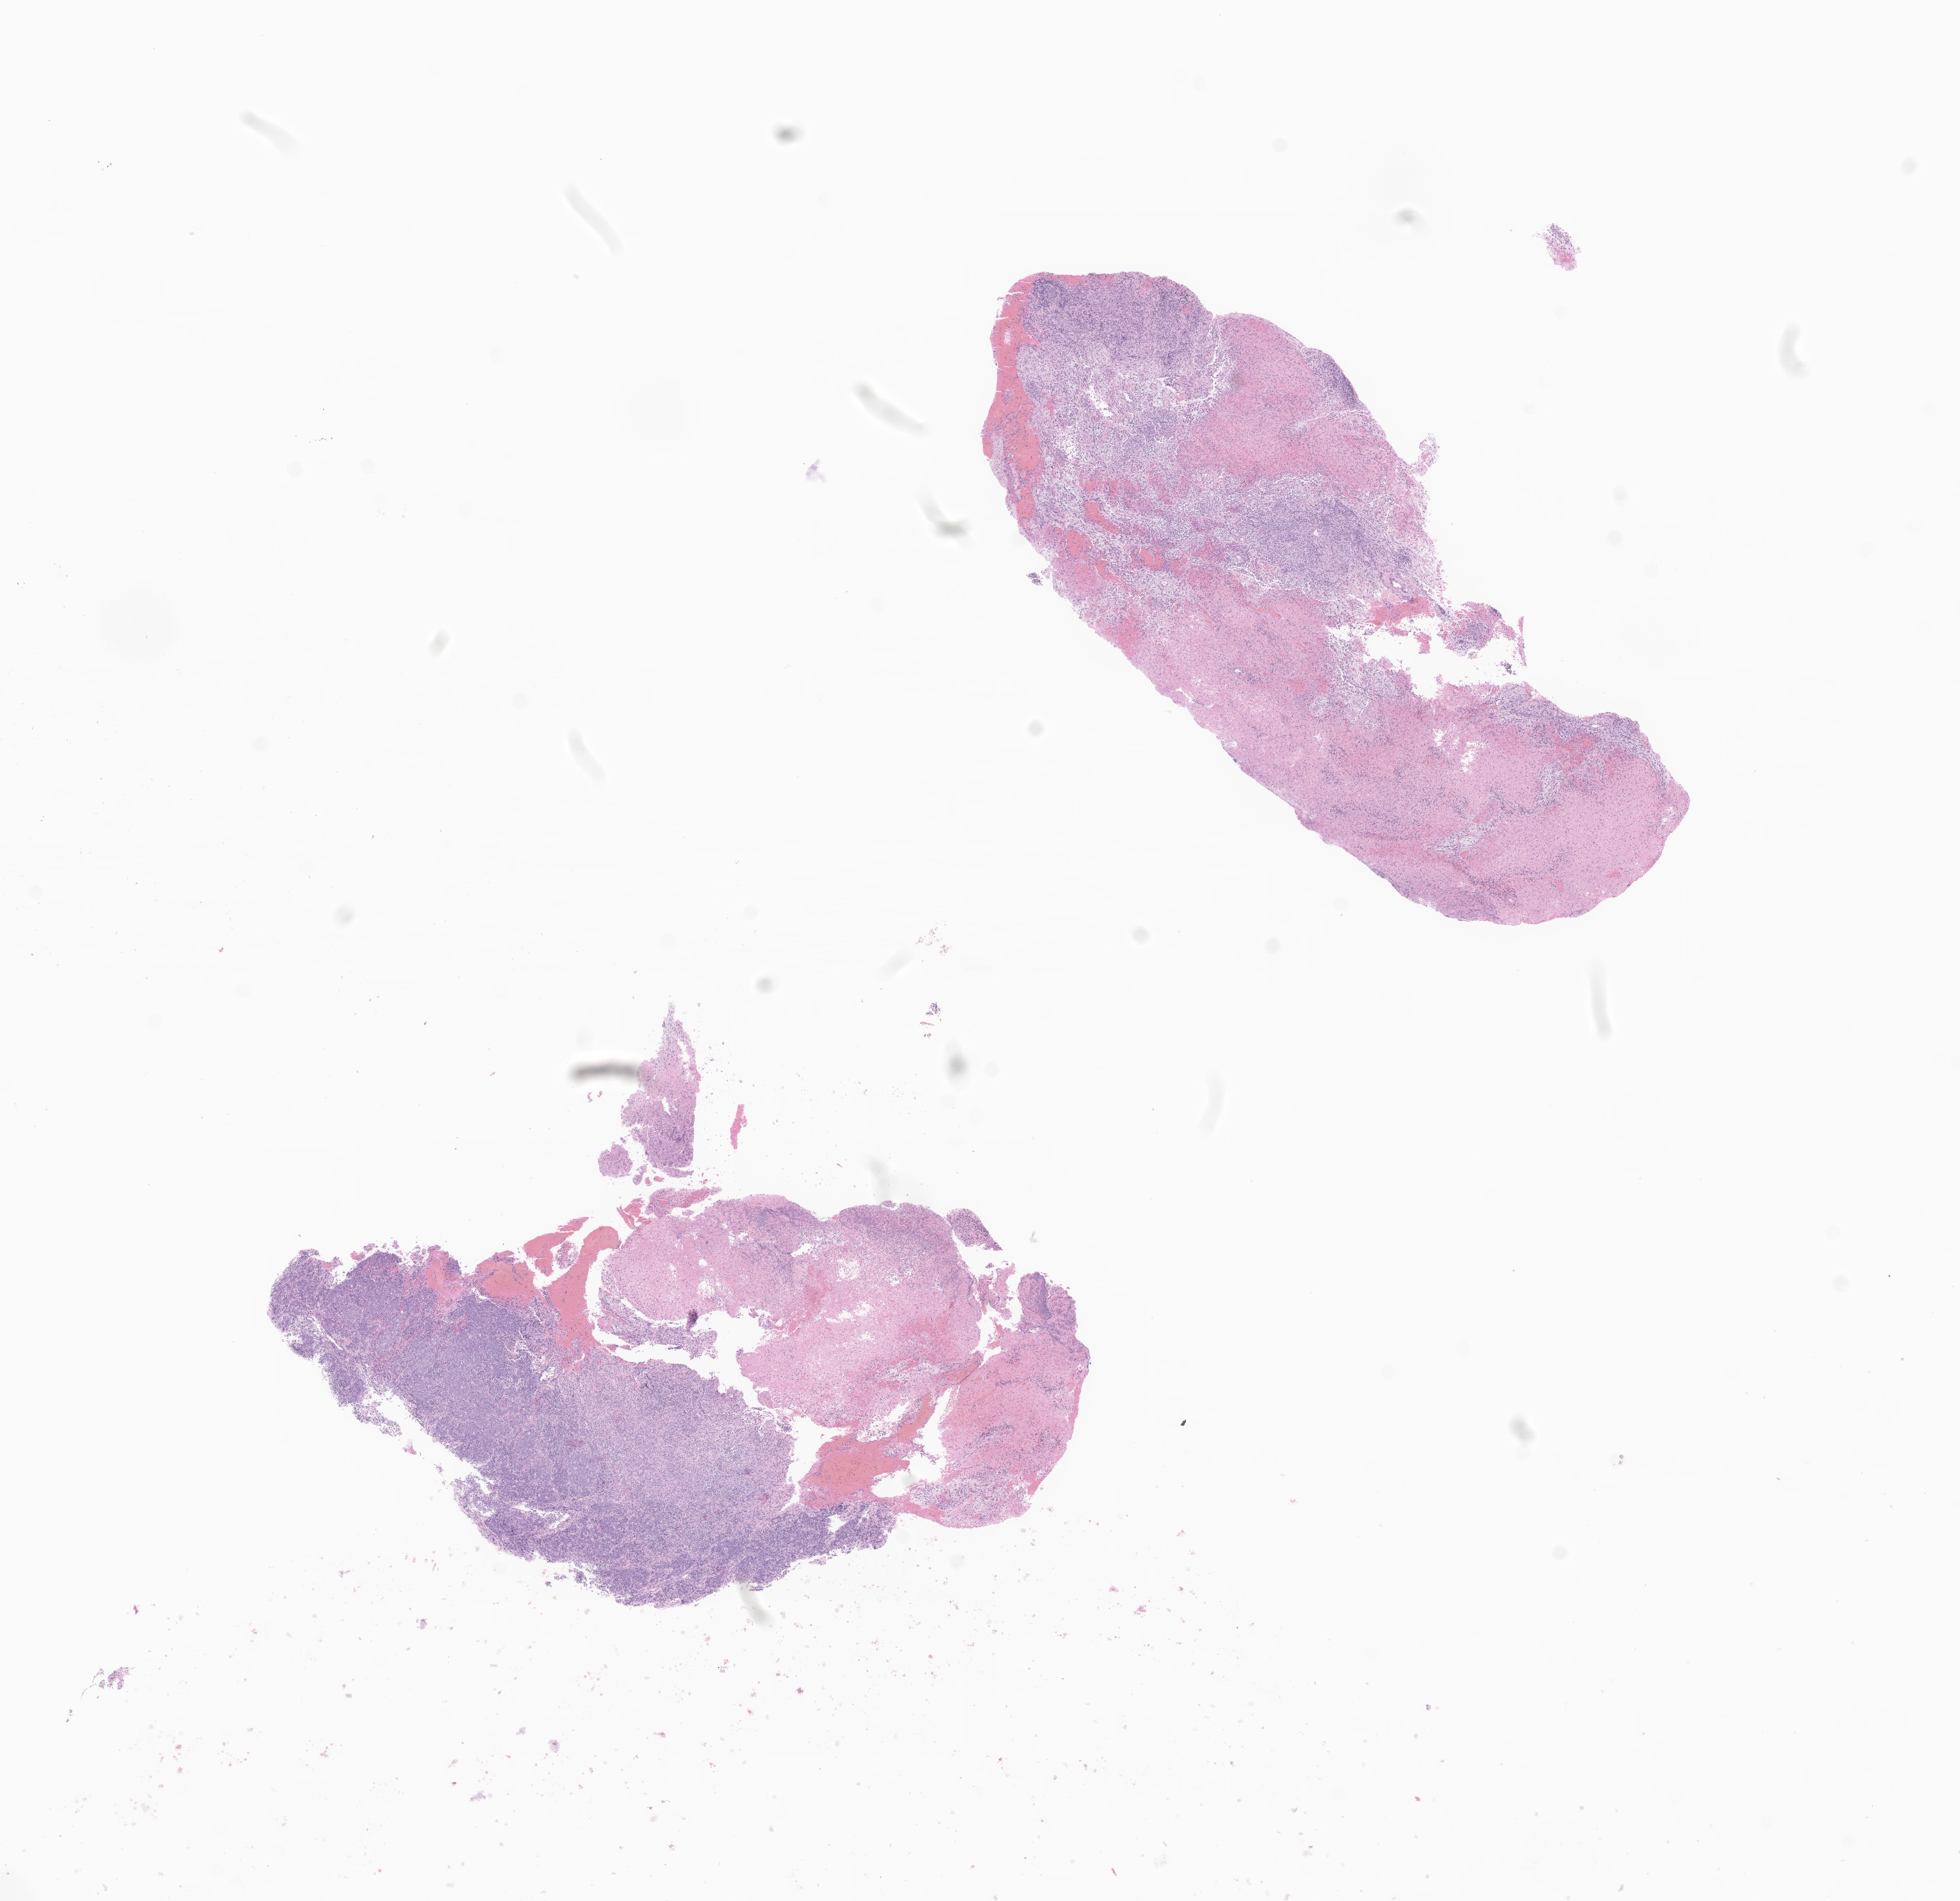
Digitized haematoxylin and eosin-stained section of tumor tissue from the nasal cavity — low-resolution overview of the scanned area, about 13.6 x 13.2 mm; FFPE section. Patient: female, age 147 months (12 years 3 months).
• recorded diagnosis: Carcinoma, NOS